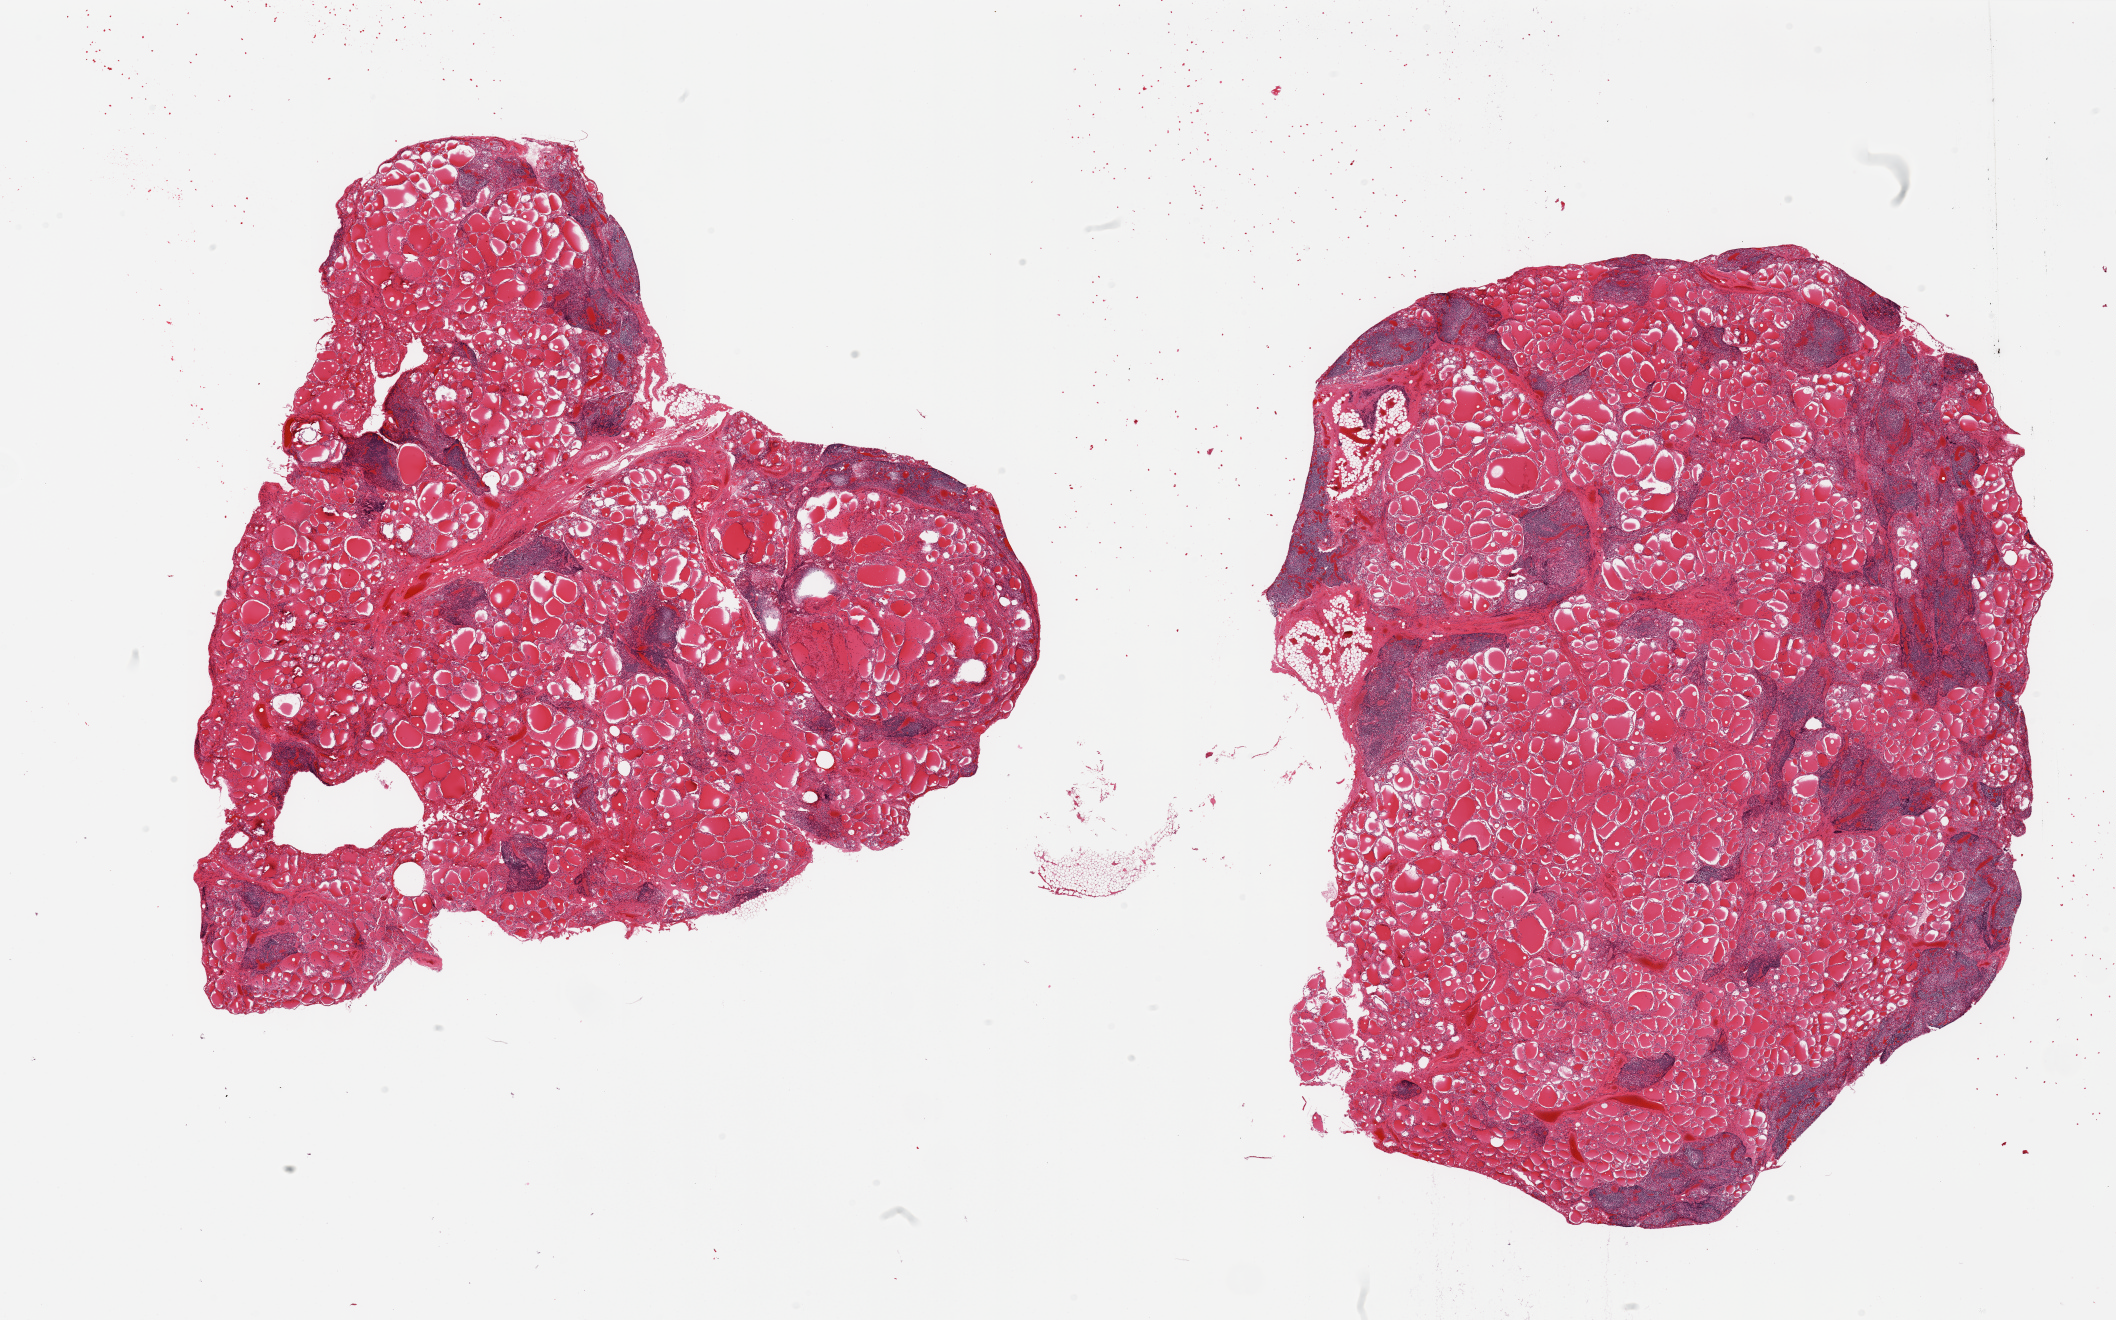
Haematoxylin and eosin whole-slide image, shown as a low-resolution overview of the whole scanned area (about 33.5 x 20.9 mm, from a 20x scan), PAXgene-fixed, paraffin-embedded tissue, section of thyroid (target tissue), tissue donor sample. Donor sex: male.
Review note (as recorded): 2 pieces; moderate lymphocytic infiltrate (Hashimoto thyroiditis).